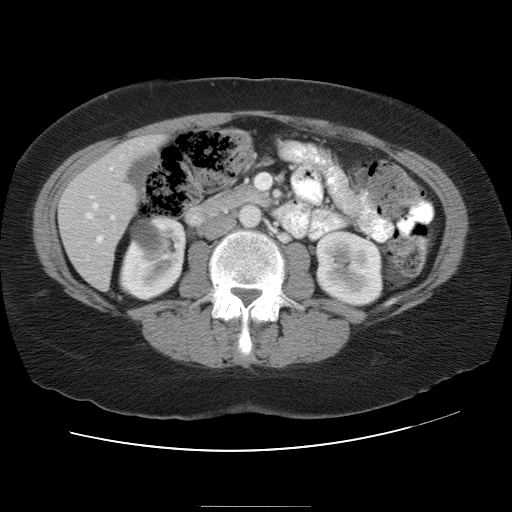
Contrast-enhanced abdominal CT, one axial slice. Position 11 of 30 along the scan axis. 120 kVp. Intravenous contrast given. Soft-tissue window (W 400 / L 40 HU). 7.5 mm slice thickness. 512 × 512 image matrix, field of view 376 × 376 mm. Female patient, age 52 years. Case-level facts recorded for this patient, not image findings: diagnosis: colorectal cancer liver metastases, imaged before liver resection.
Structures marked on this image (expert manual segmentation):
- hepatic veins: box from (x=86, y=204) to (x=97, y=219) px
- liver: (x=59, y=137)–(x=164, y=289)
- portal vein (with intrahepatic branches): (x=90, y=168)–(x=114, y=242)